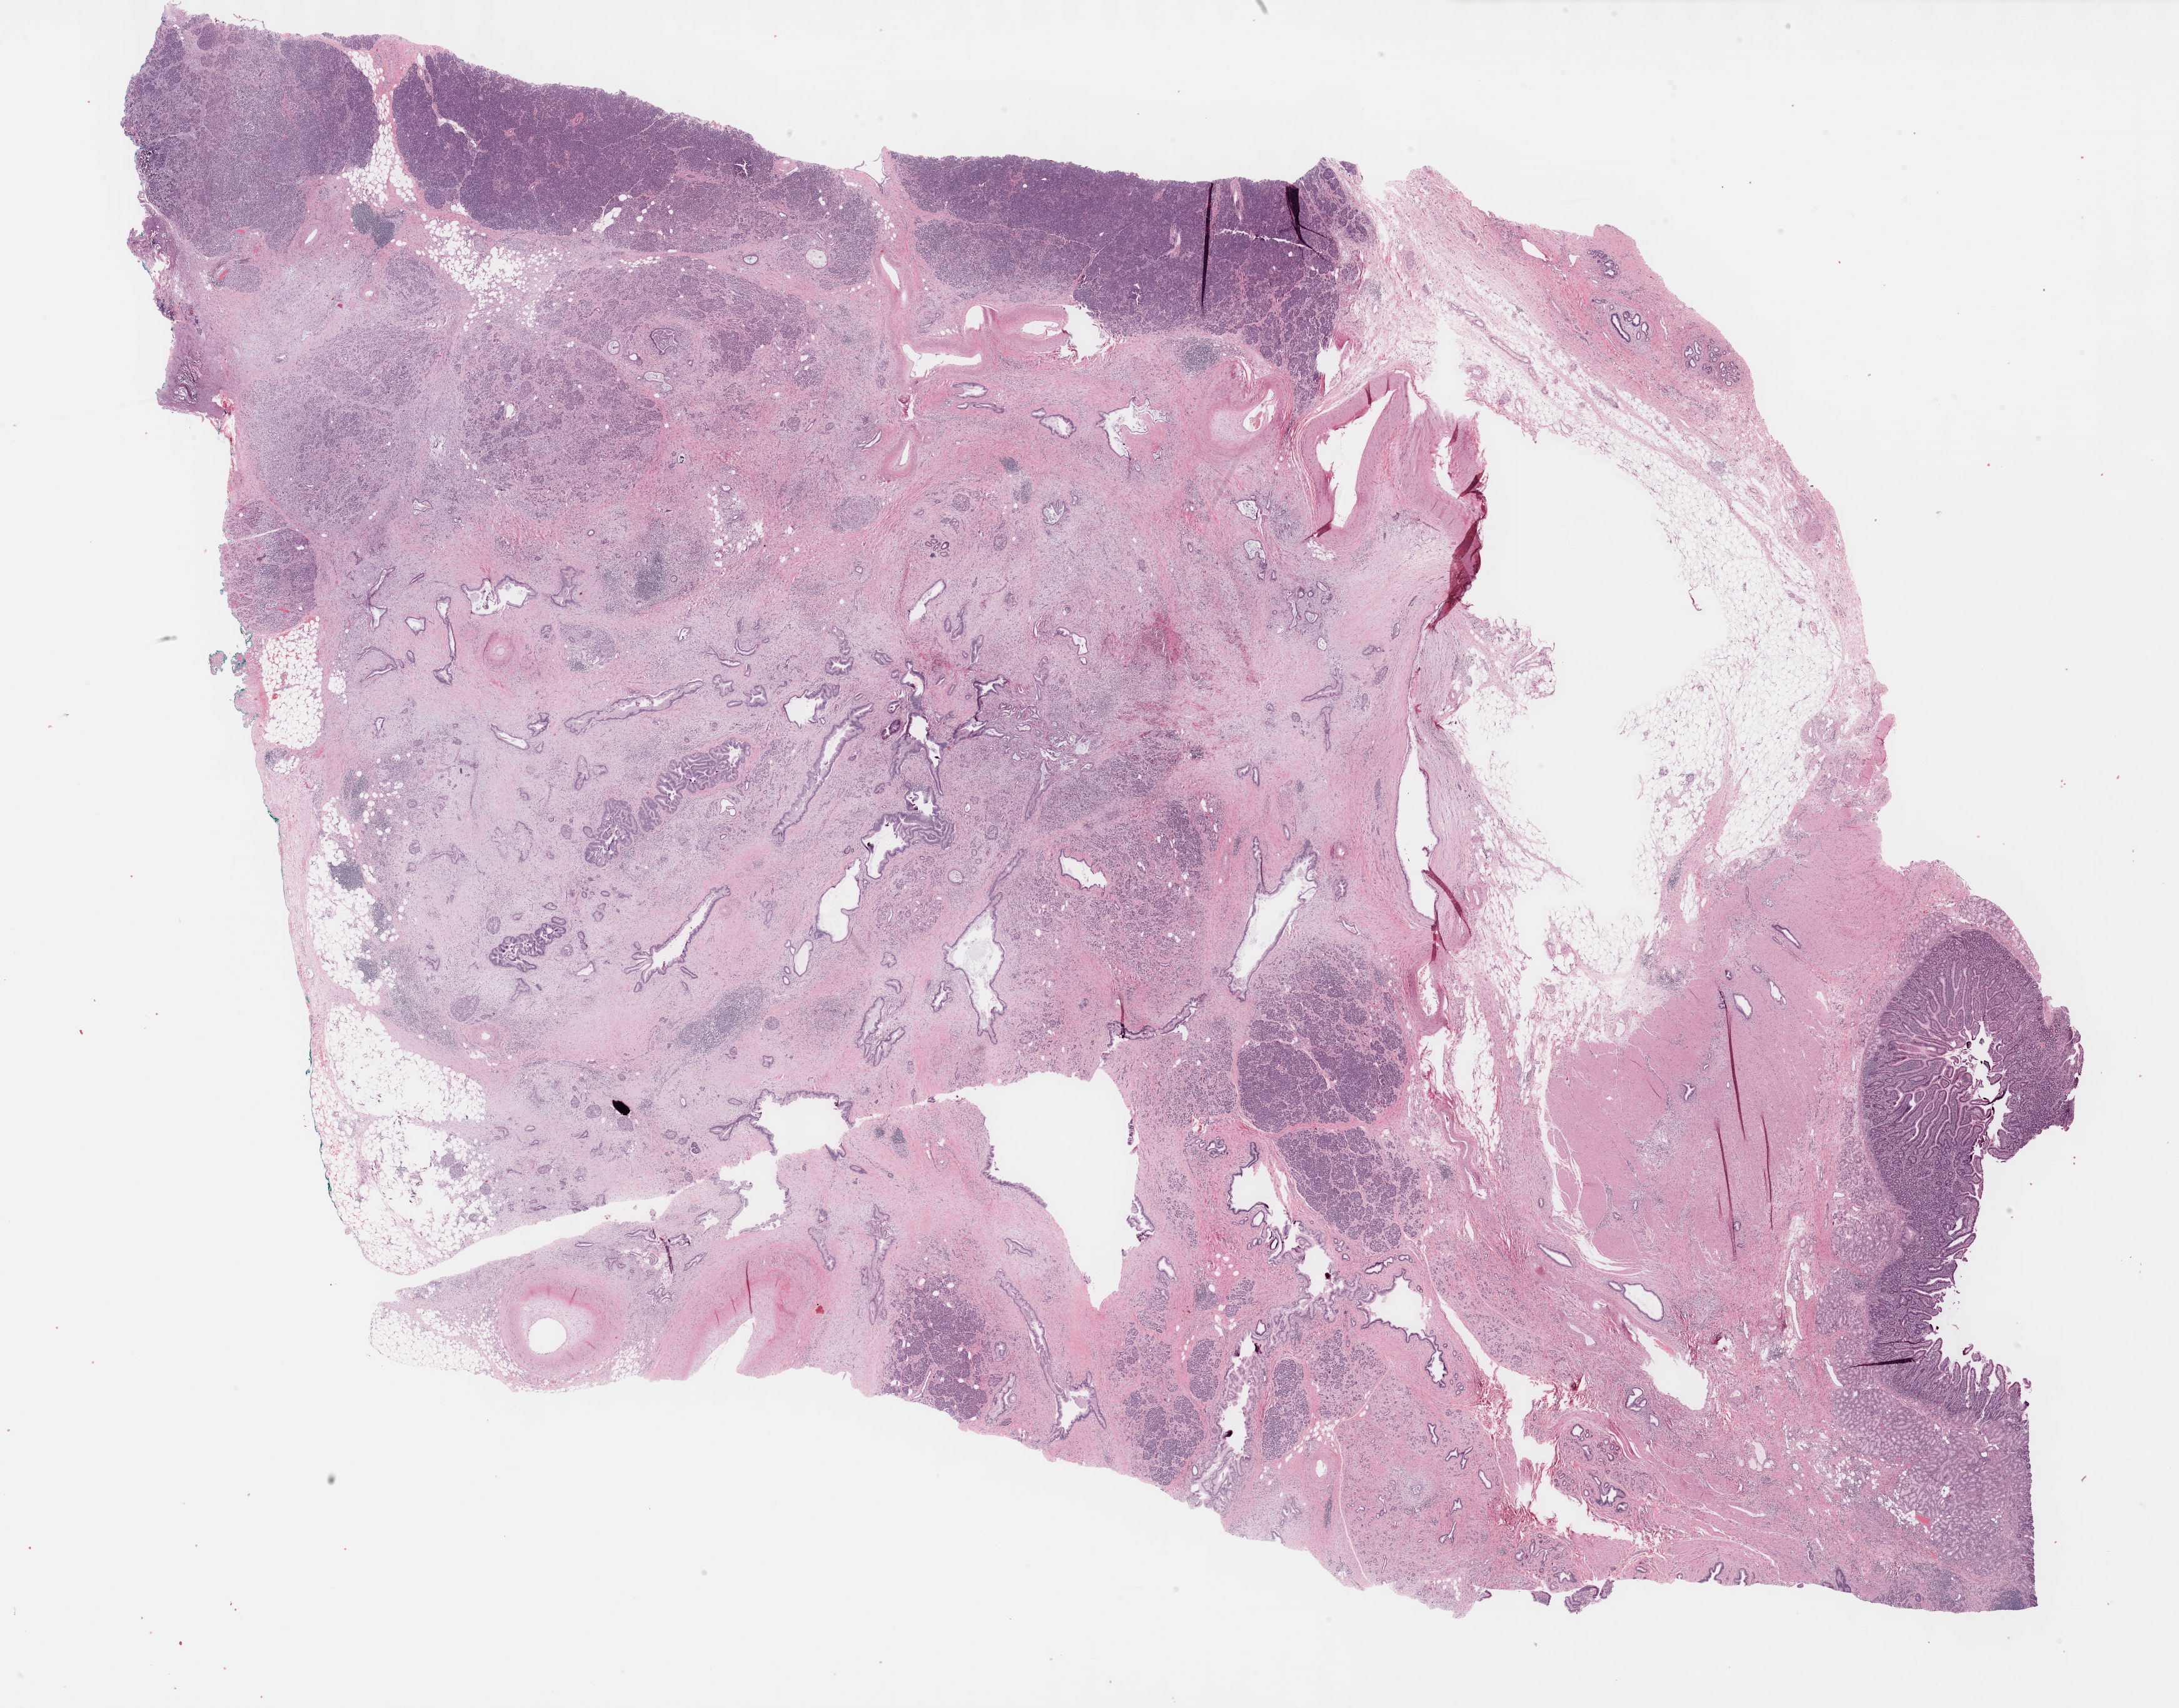
H&E whole-slide image — a low-resolution overview of the entire scanned area, about 28.2 x 22.1 mm (from a 40x scan). Formalin-fixed paraffin-embedded (FFPE) diagnostic section. Pancreas, primary tumour sample. Patient: male, age at initial diagnosis 76 years. Histologic grade: G3 (poorly differentiated).
* lymph nodes positive (case pathology): 1 of 1 examined
* AJCC pathologic stage: IIB
* pathologic diagnosis: Infiltrating duct carcinoma, NOS (head of pancreas)